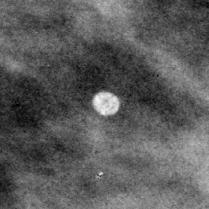
Region of interest cut from a scanned film mammogram (one marked finding); left breast; MLO view.
Finding: calcifications, morphology lucent center; BI-RADS assessment category 2; benign without callback (not worked up further).